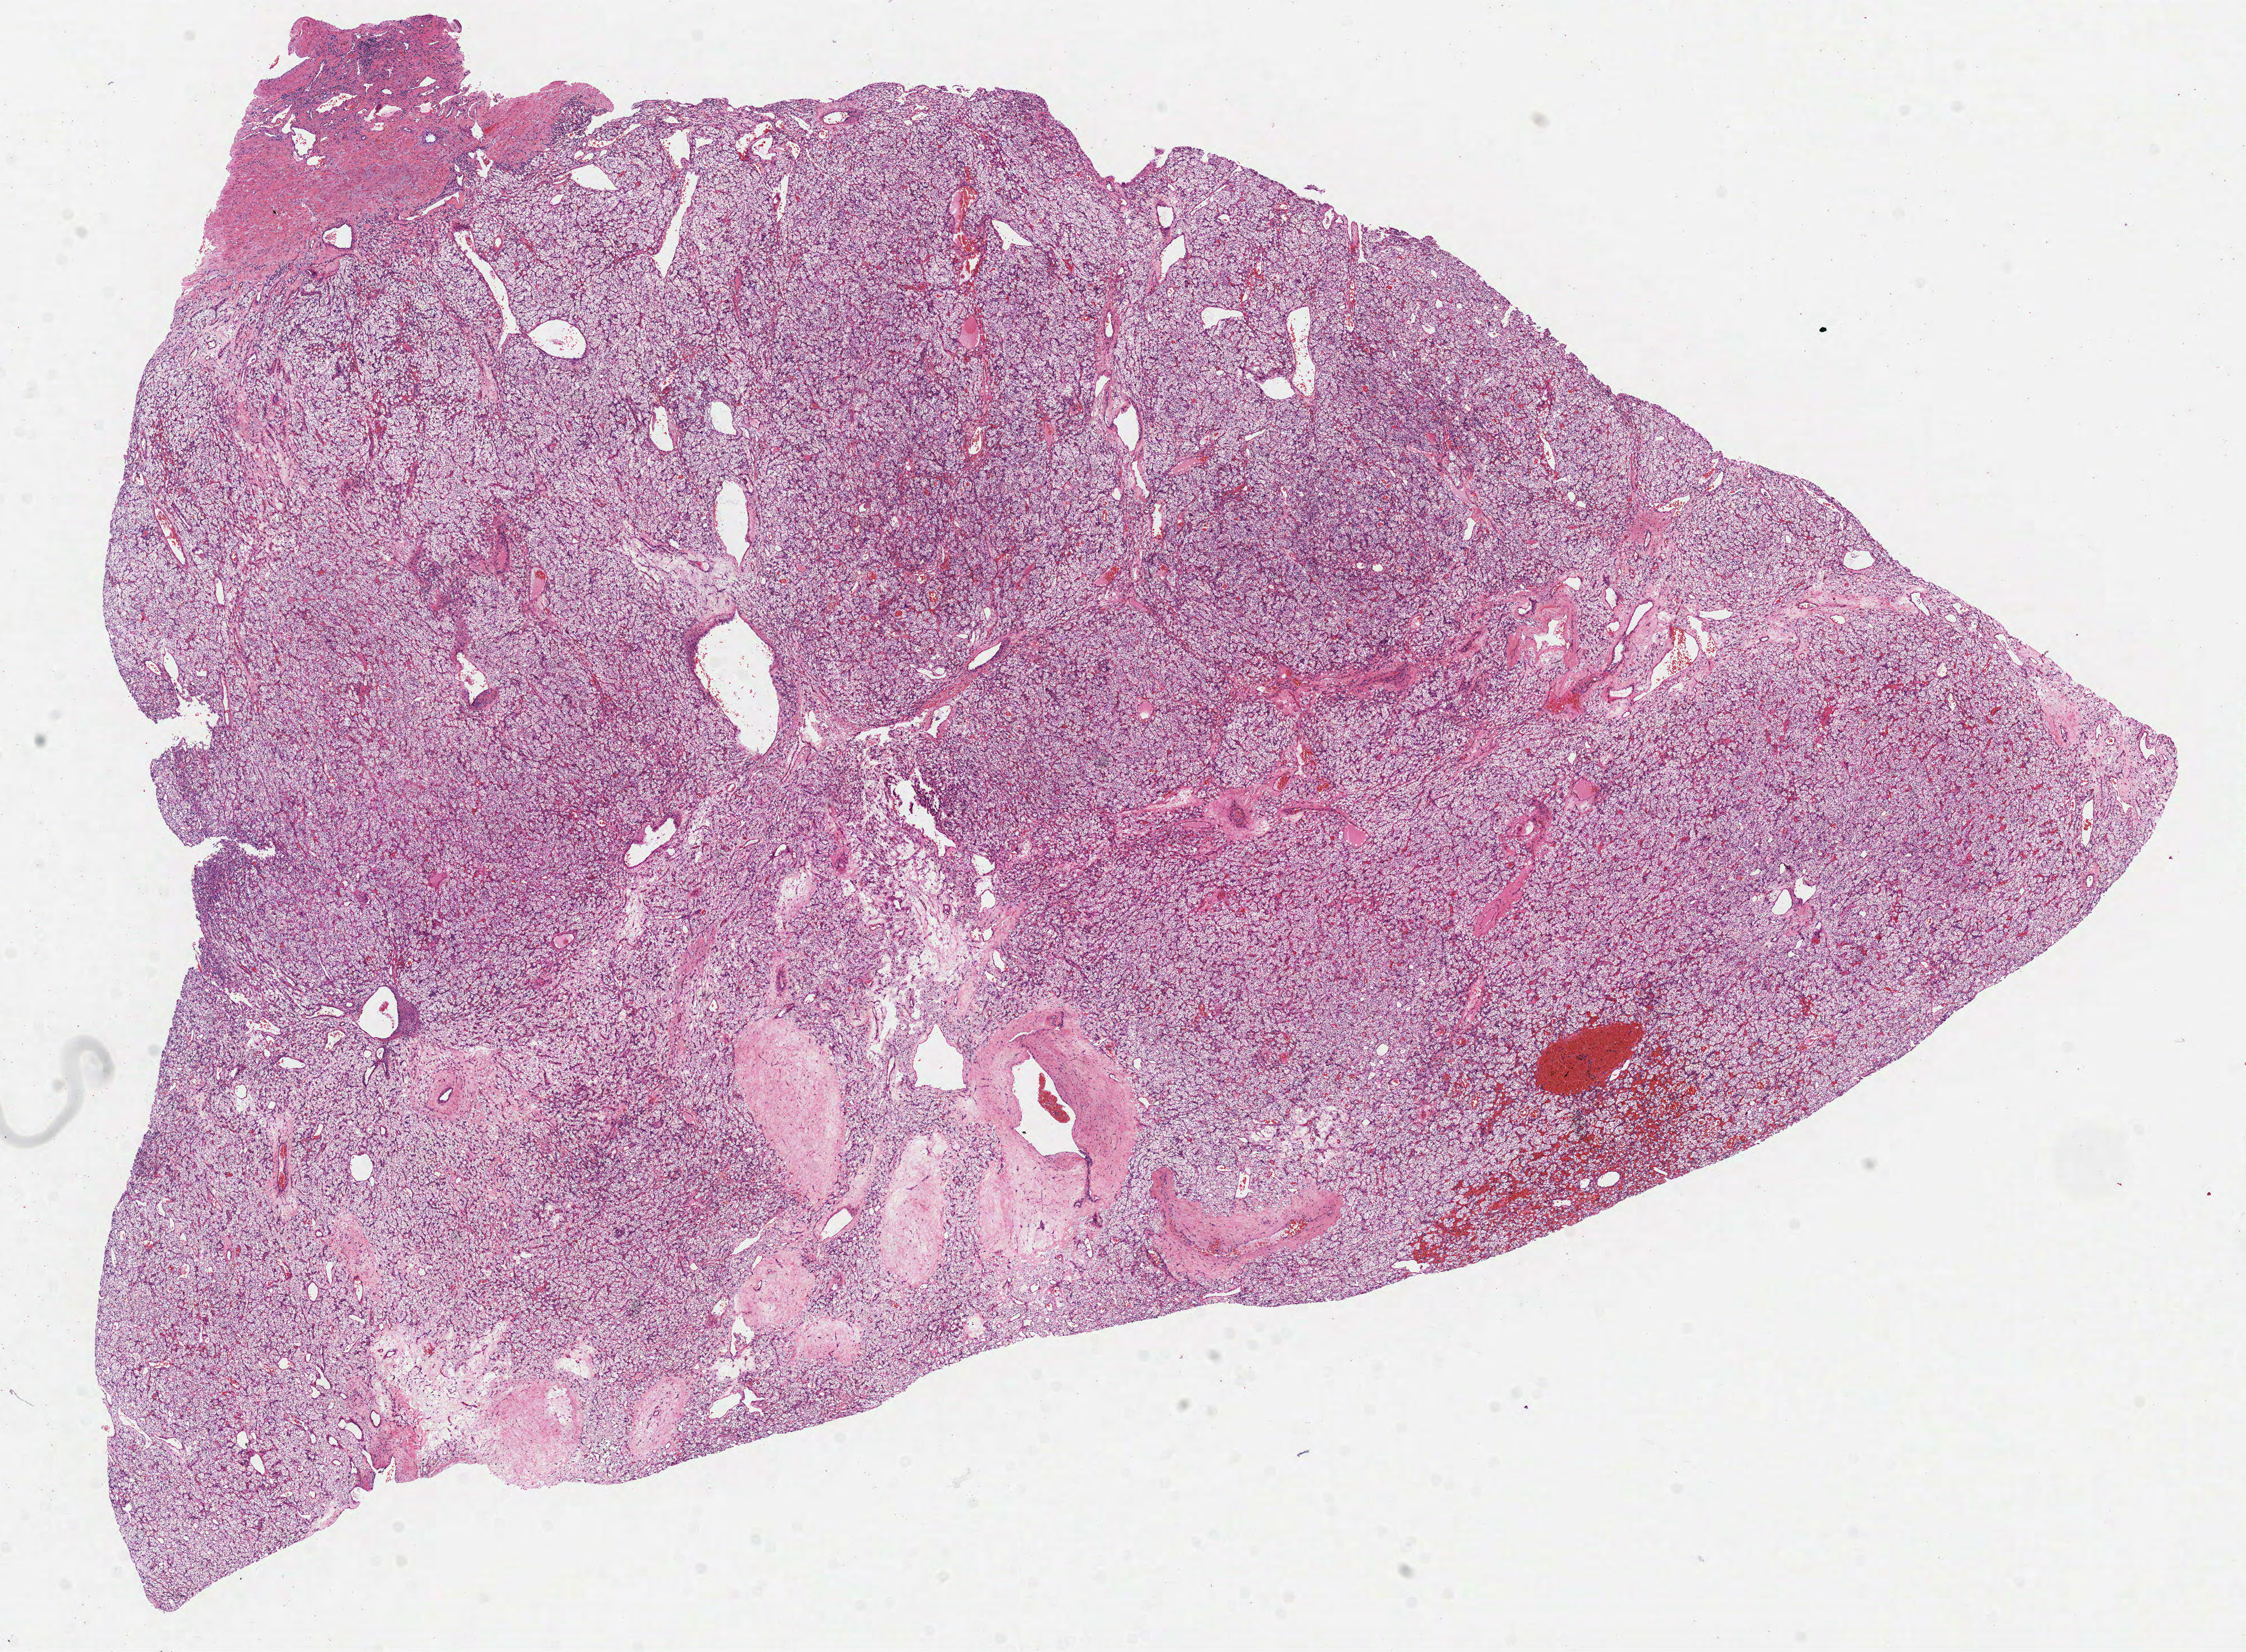
Whole-slide histology image, H&E-stained — whole scanned area (about 16.0 x 11.7 mm) shown as a low-resolution overview, FFPE section, kidney, primary tumour sample. Patient: female, age at initial diagnosis 61 years. Histologic grade: G1 (well differentiated).
- histologic diagnosis: Clear cell adenocarcinoma, NOS
- AJCC pathologic stage: II (7th edition)